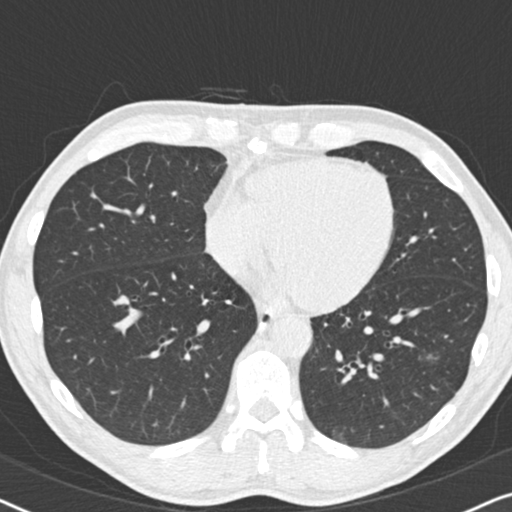
Chest CT (low-dose screening protocol), one axial image; second screening round (one year after baseline); lung window (W 1500 / L -600 HU); slice 125 of 208 in the series. Male, age 59 years at enrolment. Current smoker at enrolment.
Expert-annotated lung lesion, box from (x=414, y=338) to (x=459, y=380) px. The screening reader recorded 2 non-calcified nodules or masses ≥4 mm on this exam (left lower lobe, right middle lobe); which of them this box marks is not recorded. Official screen result: positive, other.